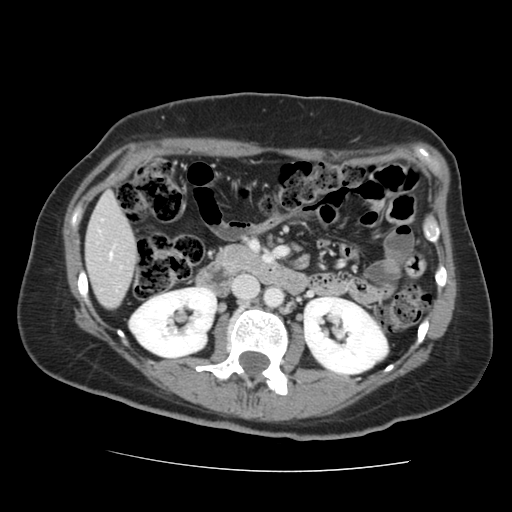
Contrast-enhanced abdominal CT, one axial slice; position 56 of 144 along the scan axis; 120 kVp; soft-tissue window (W 400 / L 40 HU); 512 × 512 image matrix. Female patient, age 46 years. Case-level facts recorded for this patient, not image findings: diagnosis: colorectal cancer liver metastases, imaged before liver resection; multiple liver metastases: no.
Structures marked on this image (expert manual segmentation):
- liver: box from (x=87, y=196) to (x=135, y=308) px
- planned liver remnant (the part of the liver to remain after resection): (x=87, y=196)–(x=135, y=308)
- portal vein (with intrahepatic branches): (x=109, y=253)–(x=113, y=259)